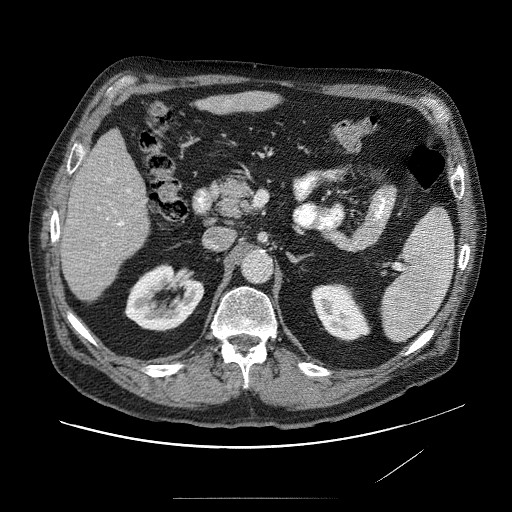
Contrast-enhanced abdominal CT (liver protocol), one axial slice; slice 30 of 89 in the series (ordered by position); reconstruction kernel STANDARD; 120 kVp; soft-tissue window (W 400 / L 40 HU); 512 × 512 image matrix, field of view 420 × 420 mm. Case-level facts recorded for this patient, not image findings: diagnosis: hepatocellular carcinoma (patient treated with transarterial chemoembolisation; whether this scan precedes or follows treatment is not stated here); TNM stage (as recorded): Stage-IVA; Child-Pugh class: A; tumour differentiation: moderately differentiated.
Structures marked on this image (semi-automatic segmentation, software-assisted and operator-edited):
- liver parenchyma outside the tumour (the mass and vessels are separate outlines, so this box may not span the whole liver): box from (x=60, y=88) to (x=290, y=308) px
- liver vessels: (x=100, y=173)–(x=135, y=252)